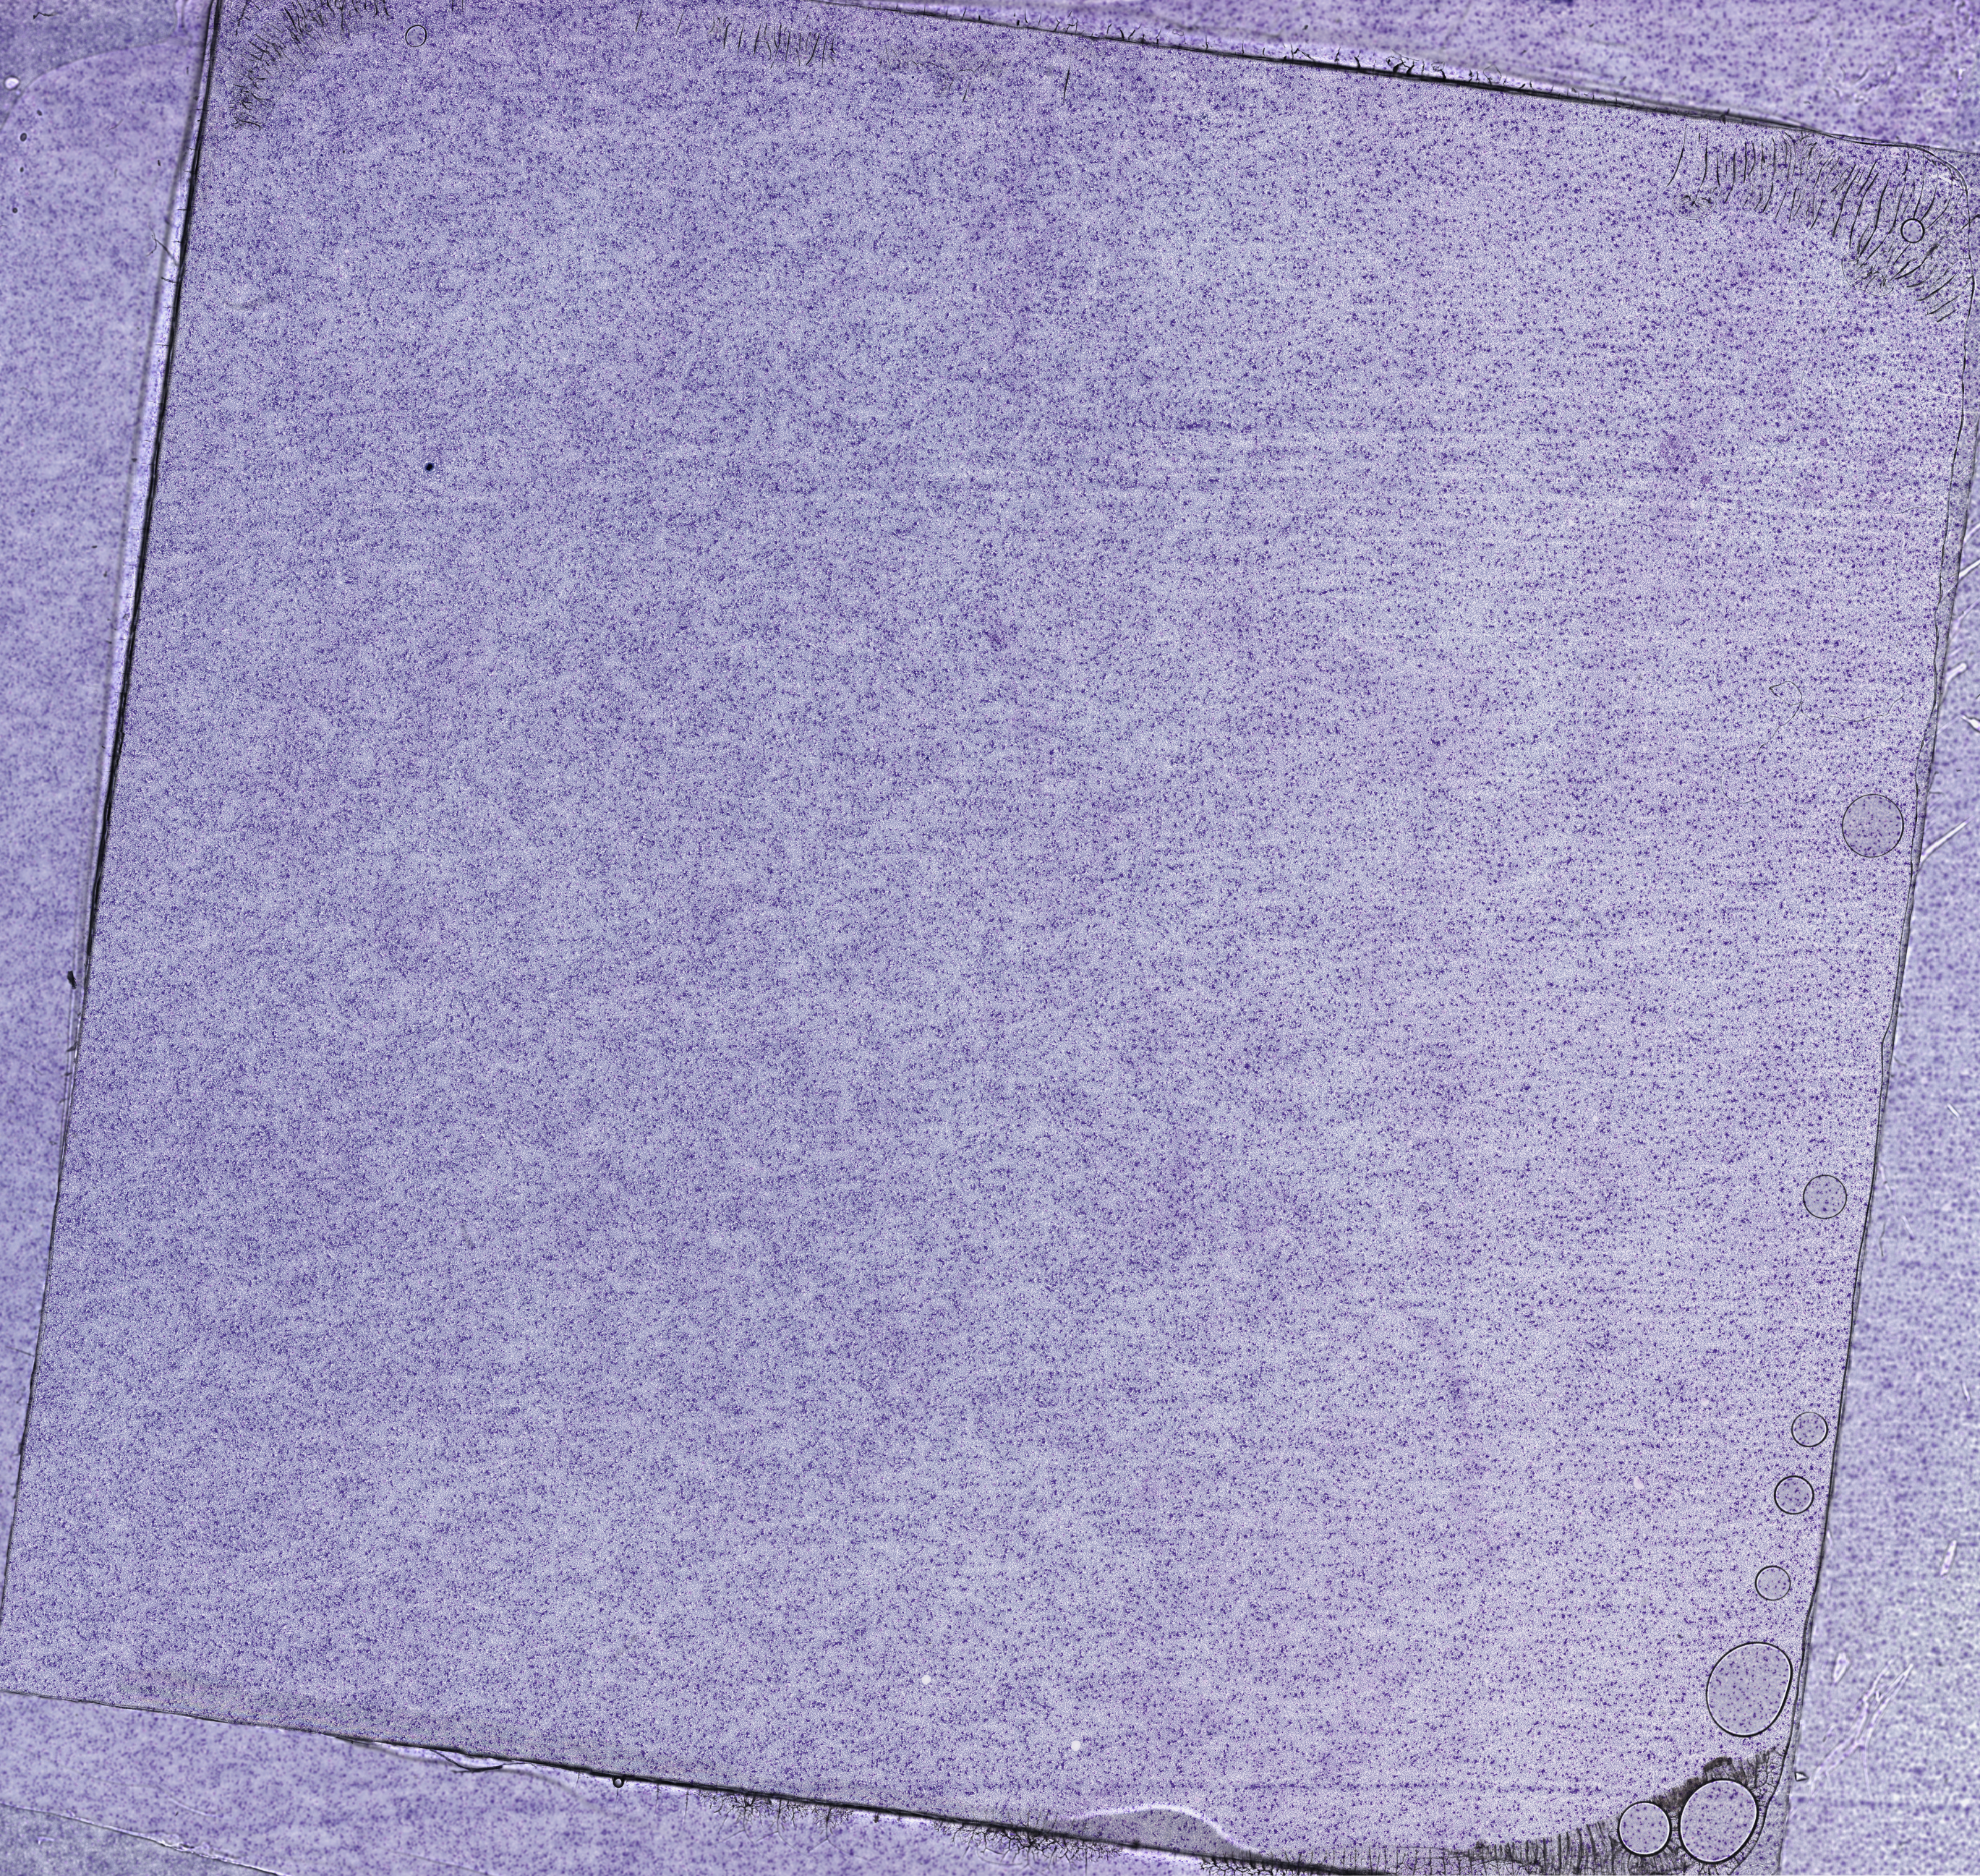
Whole-slide histology image, H&E-stained, shown as a low-resolution overview of the whole scanned area (about 22.1 x 21.0 mm). Peripheral blood (leukaemic) sample. 54-year-old male patient.
* FAB classification: M0
* diagnosis: Acute Myeloid Leukemia
* WHO classification: AML with minimal differentiation